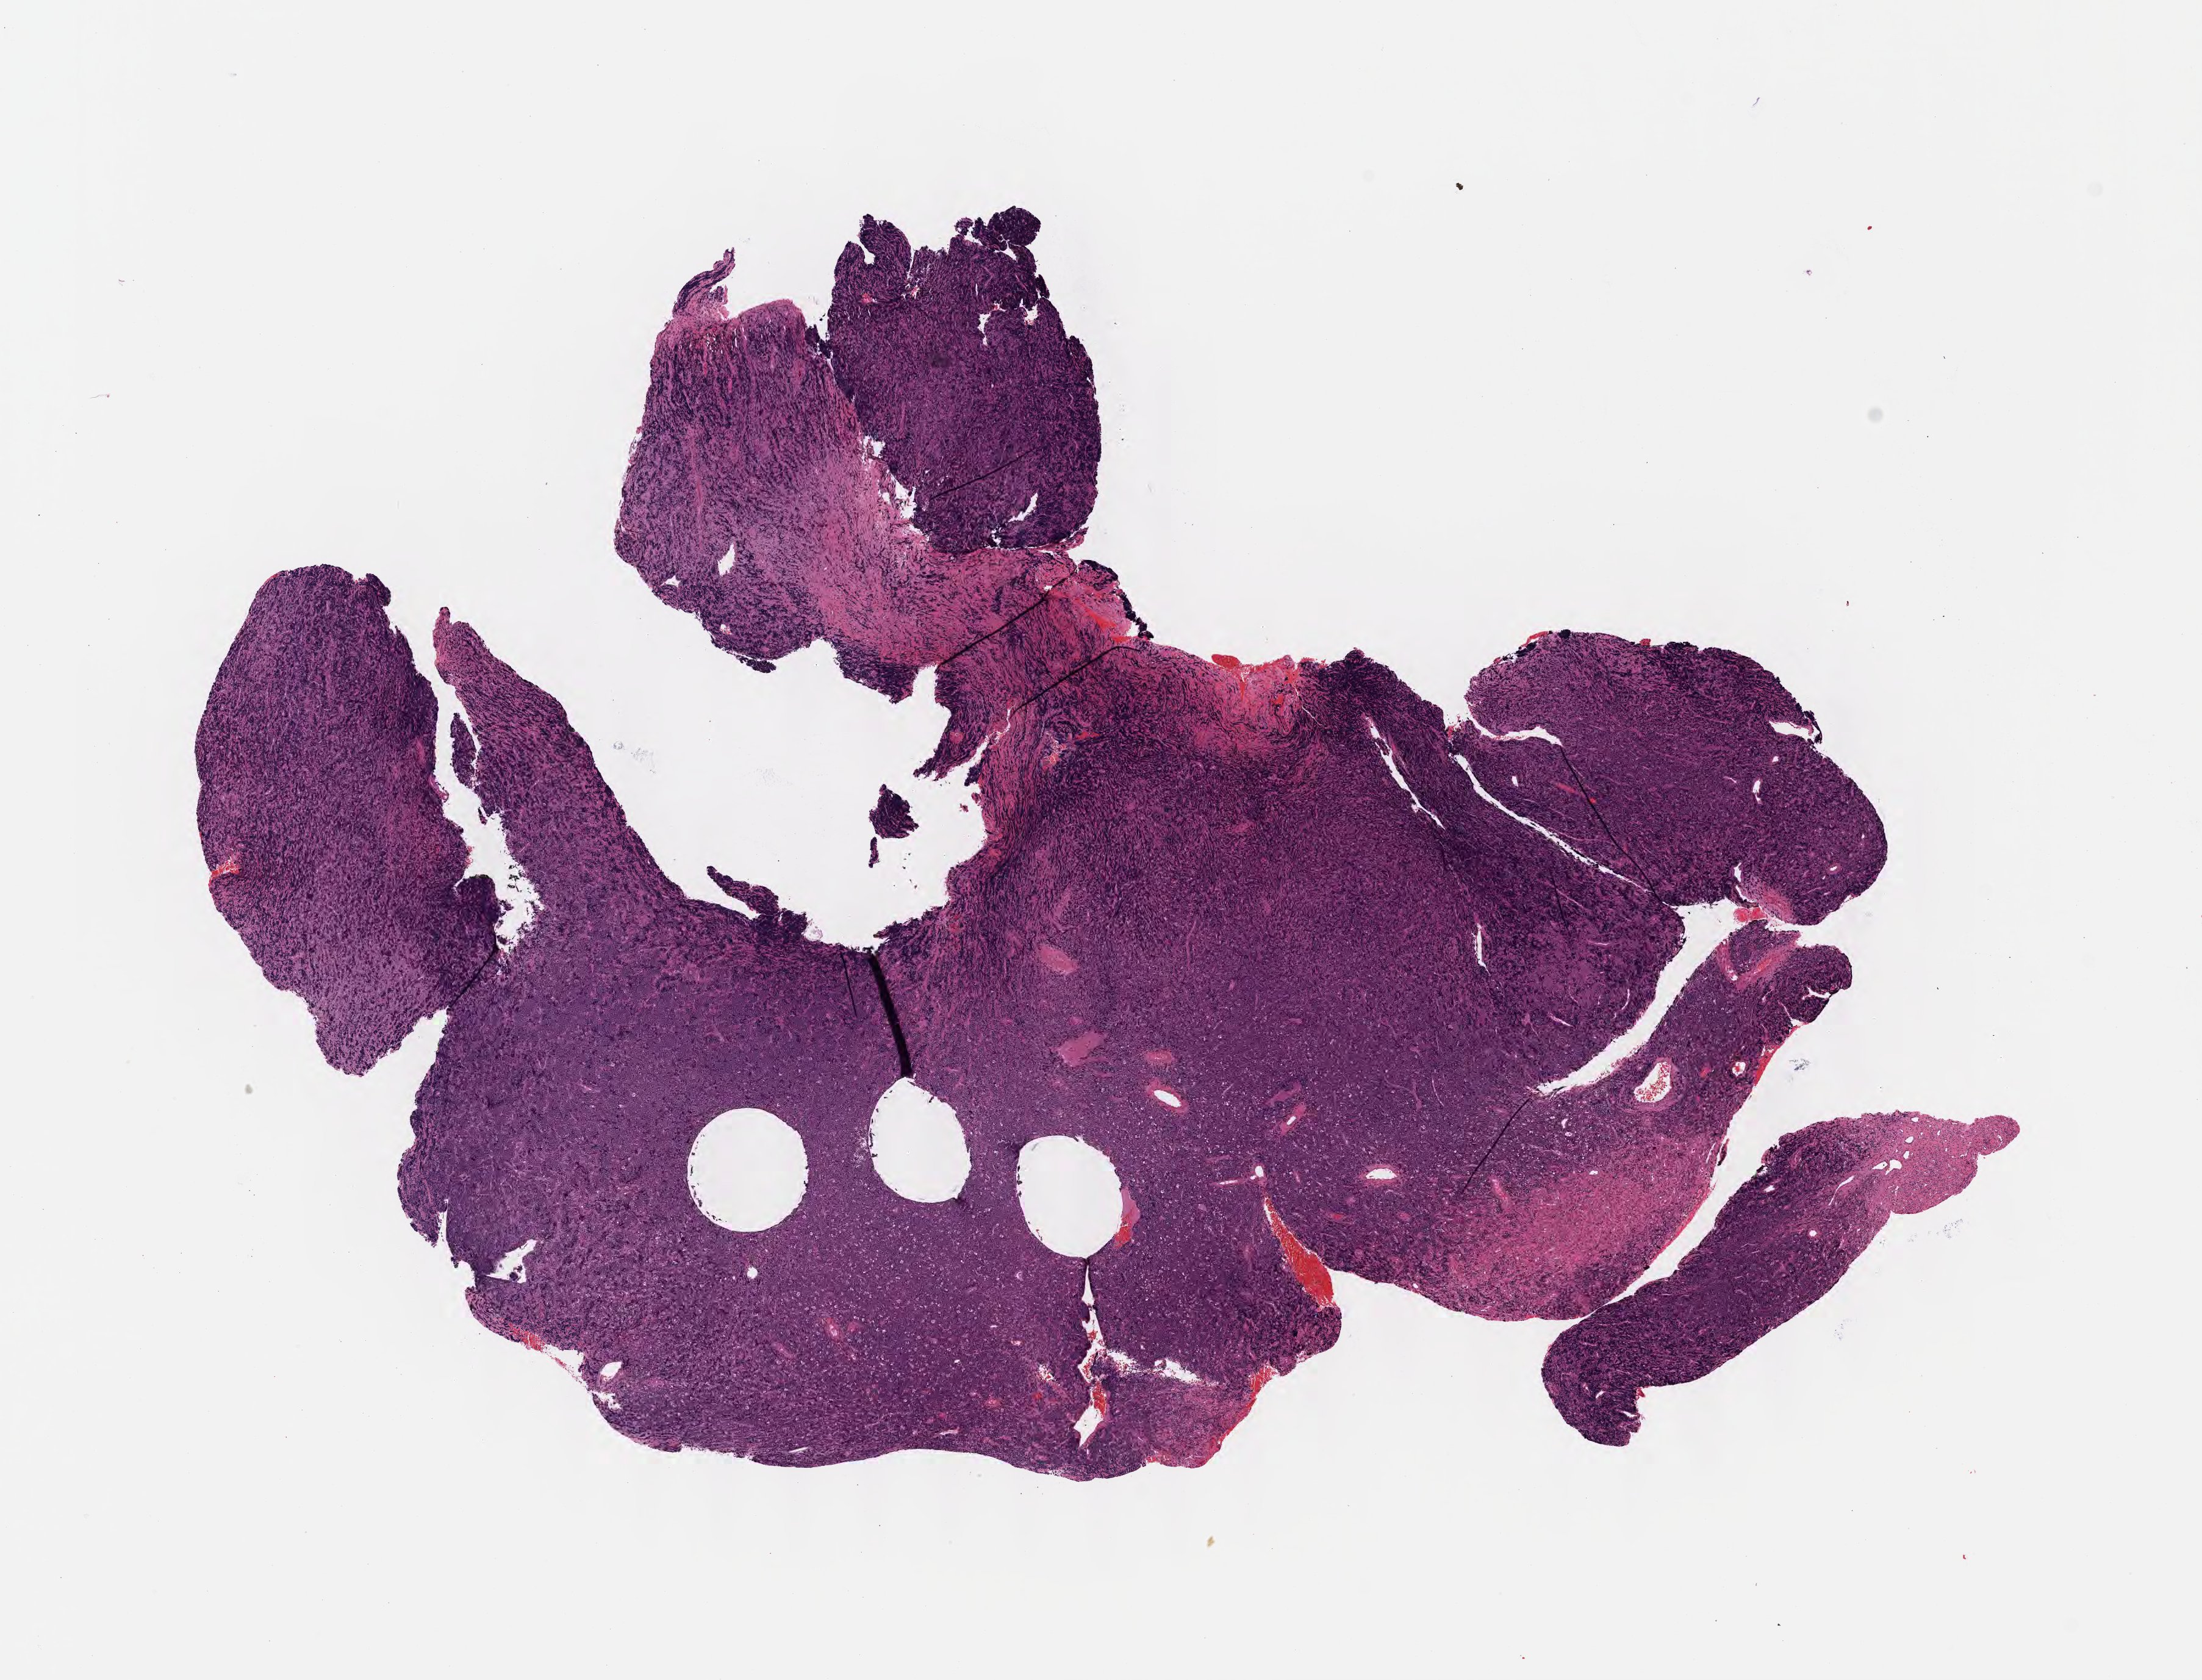
Digitized H&E-stained section, shown as a low-resolution overview of the whole scanned area (about 14.6 x 11.1 mm), formalin-fixed, paraffin-embedded (FFPE) tissue, specimen: primary tumor, anatomic site: mouth. Patient: female, age at initial diagnosis 7 years. Composition of this section per pathologist review: tumor cells 90%, tumor nuclei 90%.
Histologic diagnosis: Diffuse large B-cell lymphoma, NOS.